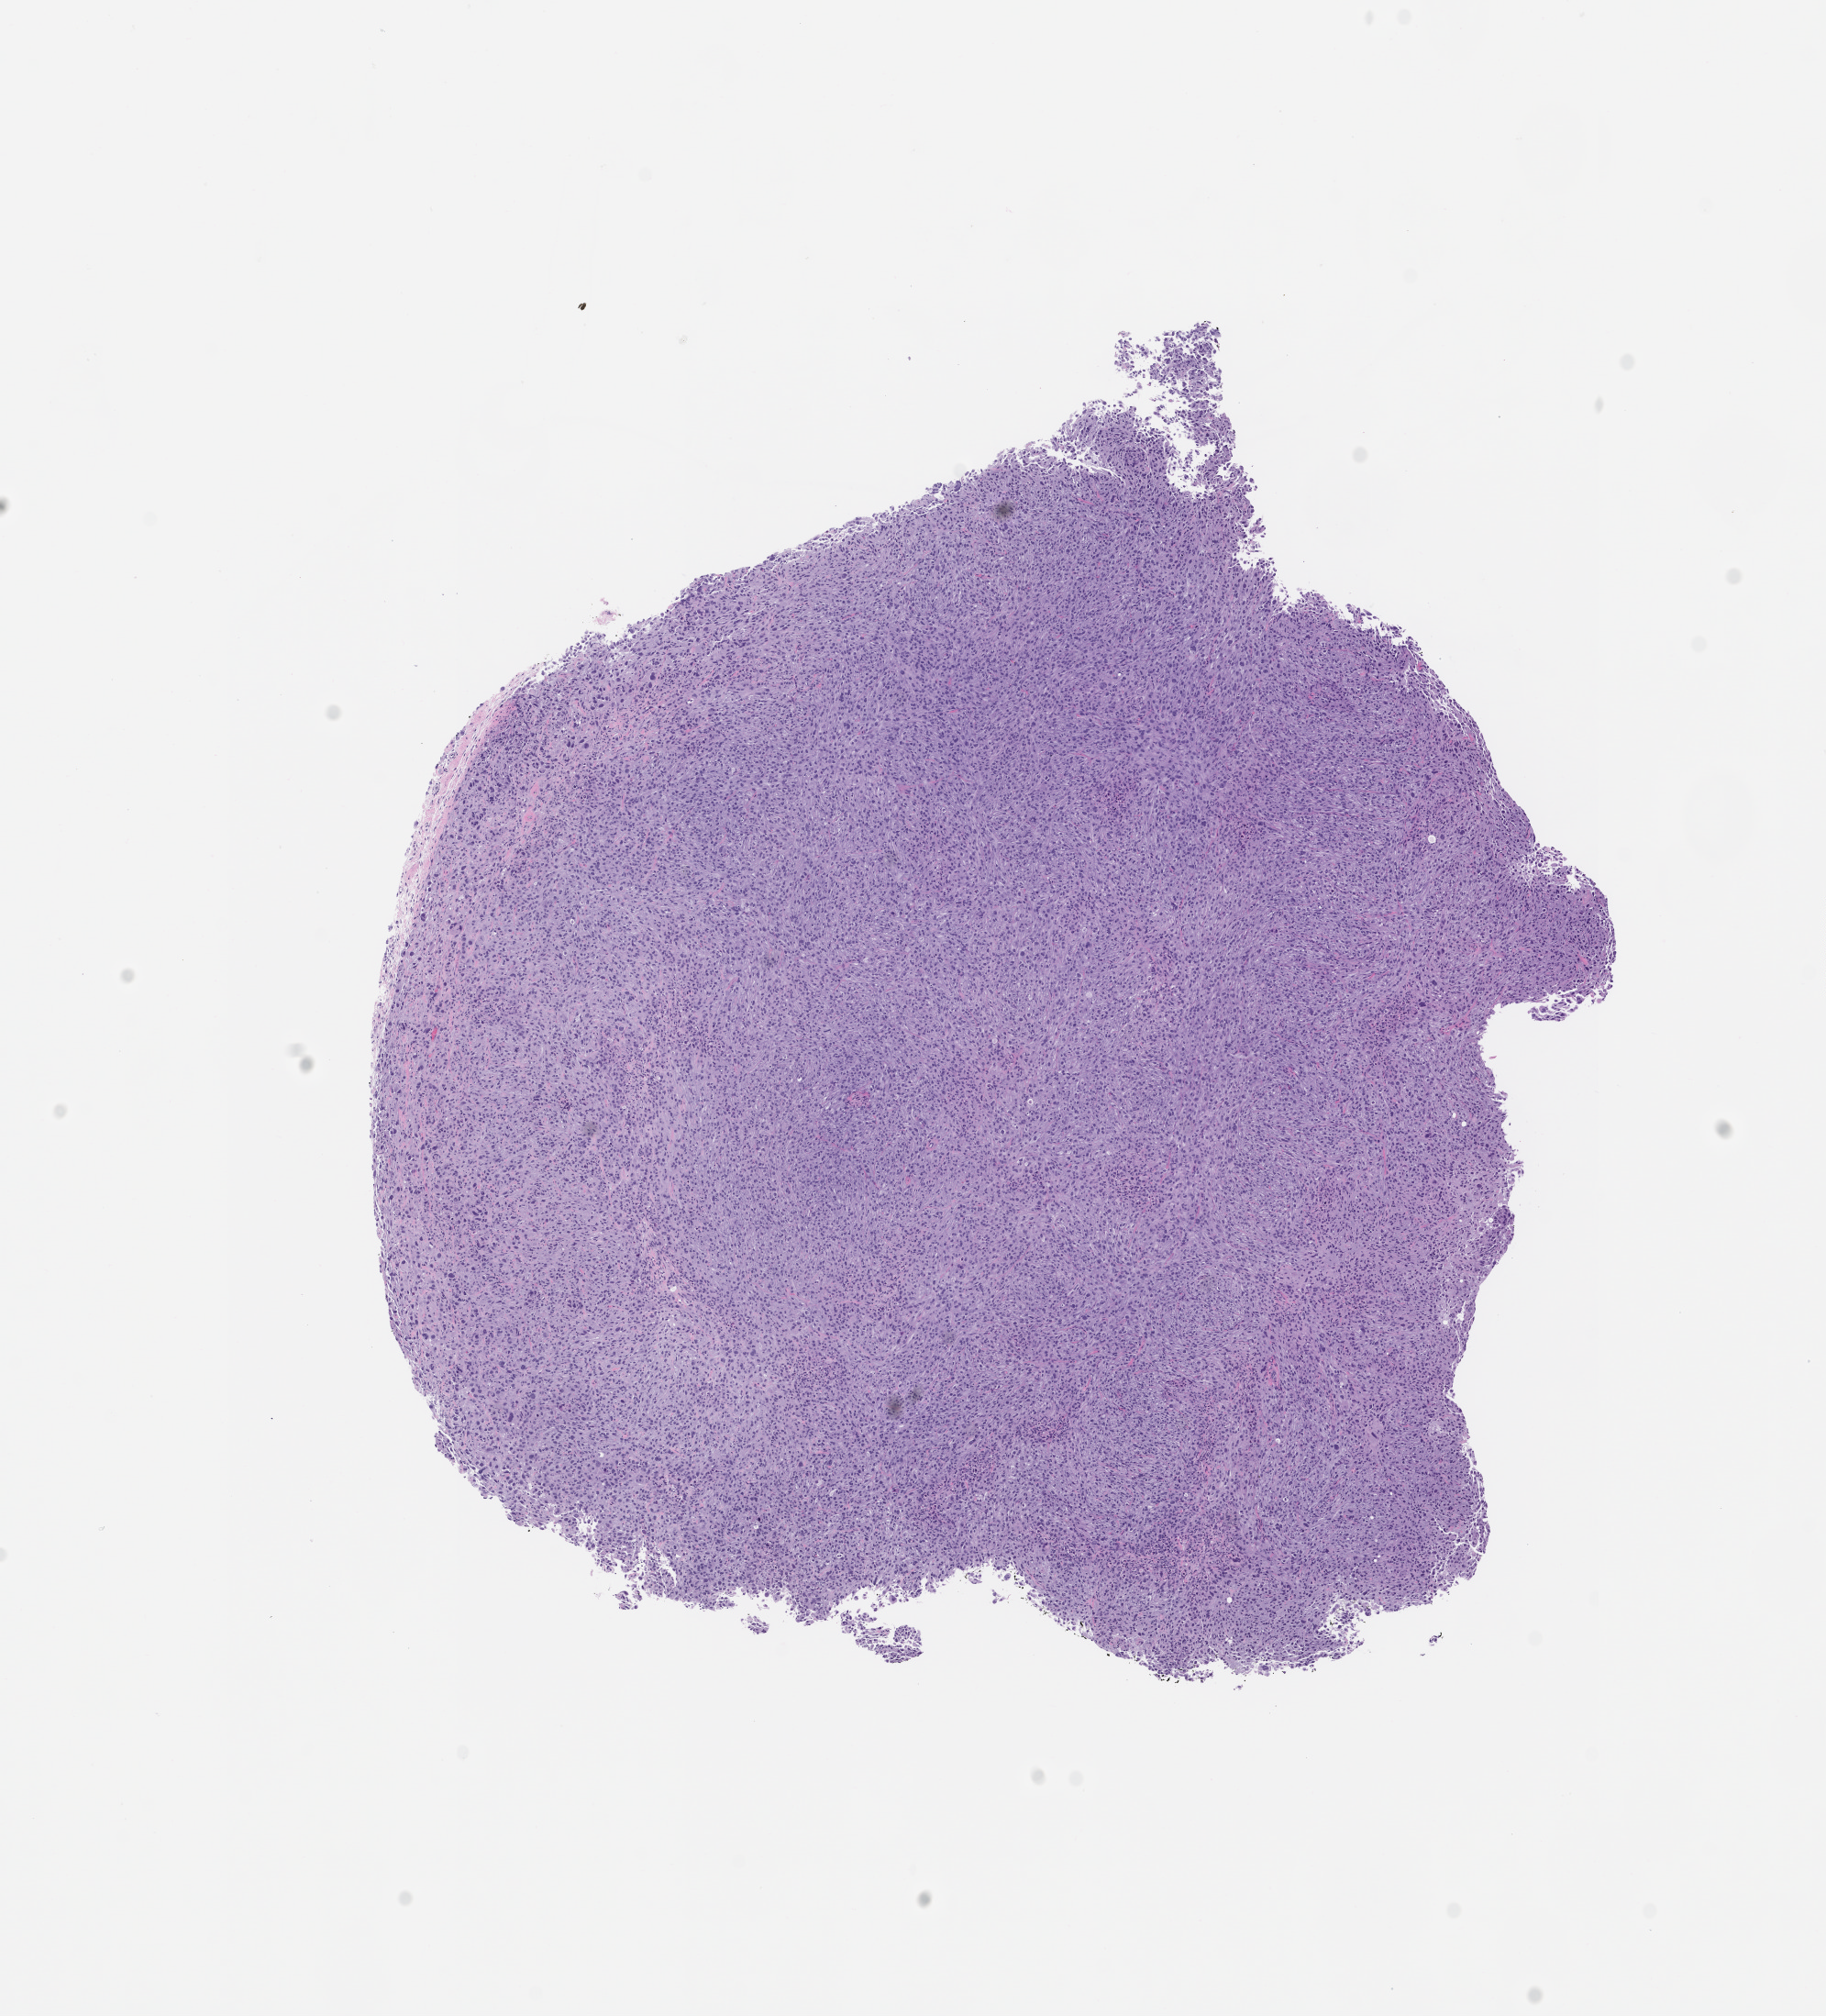
Hematoxylin and eosin (H&E) whole-slide image of a patient-derived xenograft (PDX) tumor grown in a mouse, passage 1 — shown as a low-resolution overview of the whole scanned area (about 8.0 x 8.8 mm). FFPE section. Originating tumor site category: thyroid.
• originating patient diagnosis: Thyroid Gland Oncocytic Carcinoma